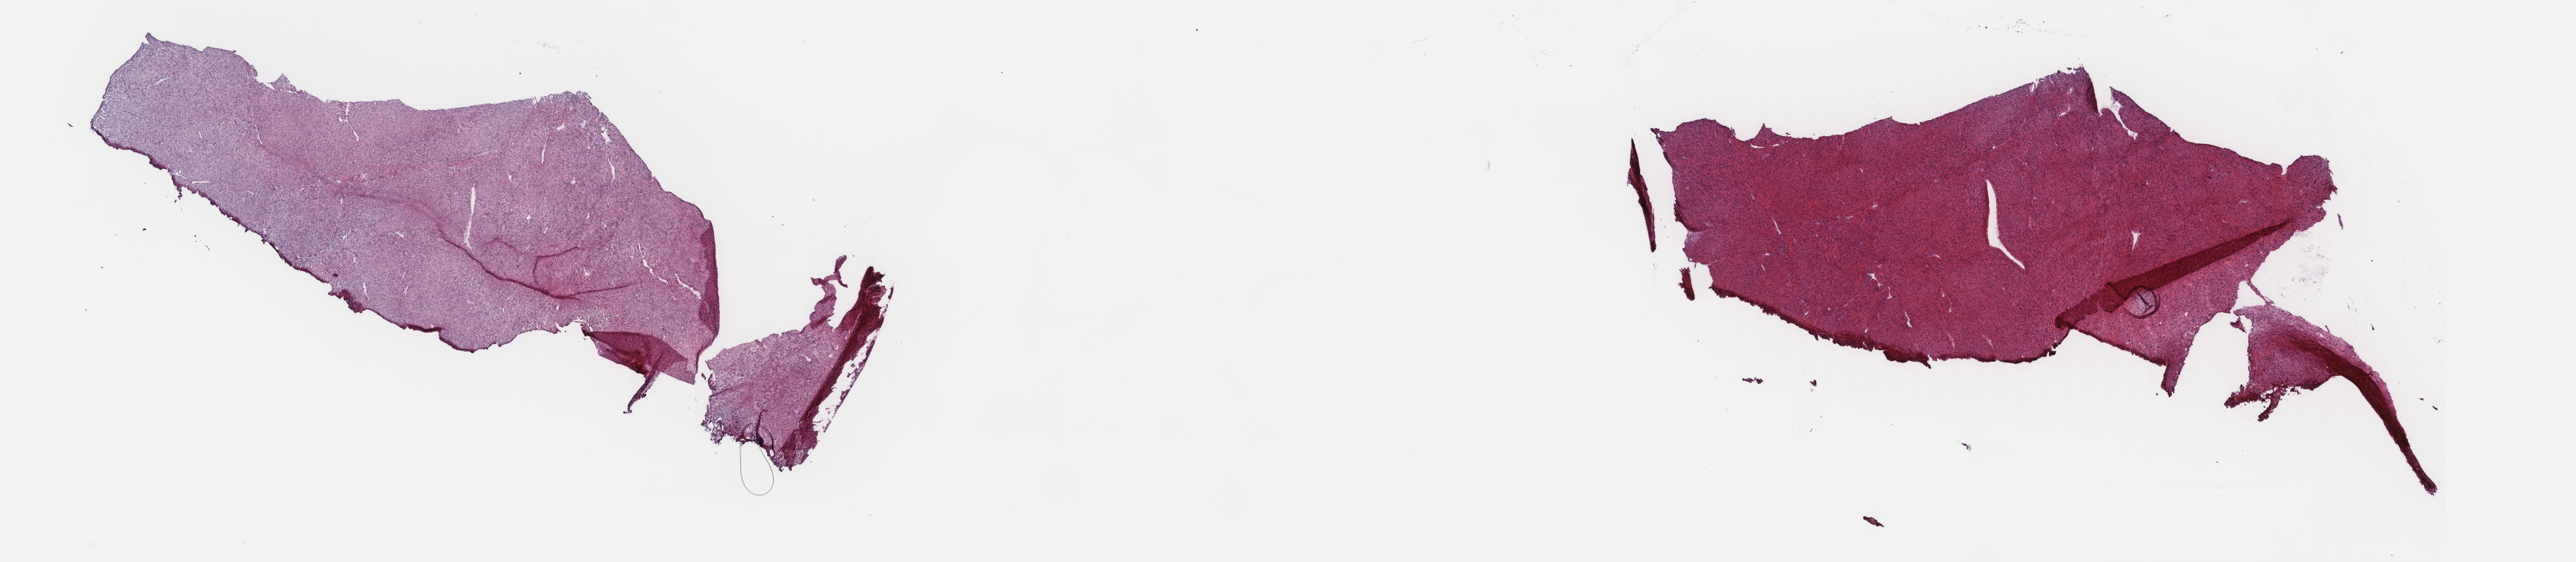
Digitized Hematoxylin and eosin (H&E) stained tissue section (whole slide) — a low-resolution overview of the entire scanned area, about 28.1 x 6.1 mm (slide scanned at 40x), frozen section from the top of the tissue portion, sample: primary tumour, retroperitoneum and peritoneum. Female, age 57 years at initial diagnosis. Composition of this section per pathologist review: tumour cells 85%, tumour nuclei 100%, normal cells 0%, stromal cells 15%, necrosis 0%. Infiltration values recorded for this section: lymphocyte infiltration 1%, monocyte infiltration 0%, neutrophil infiltration 0%.
Histologic diagnosis: Leiomyosarcoma, NOS (retroperitoneum).